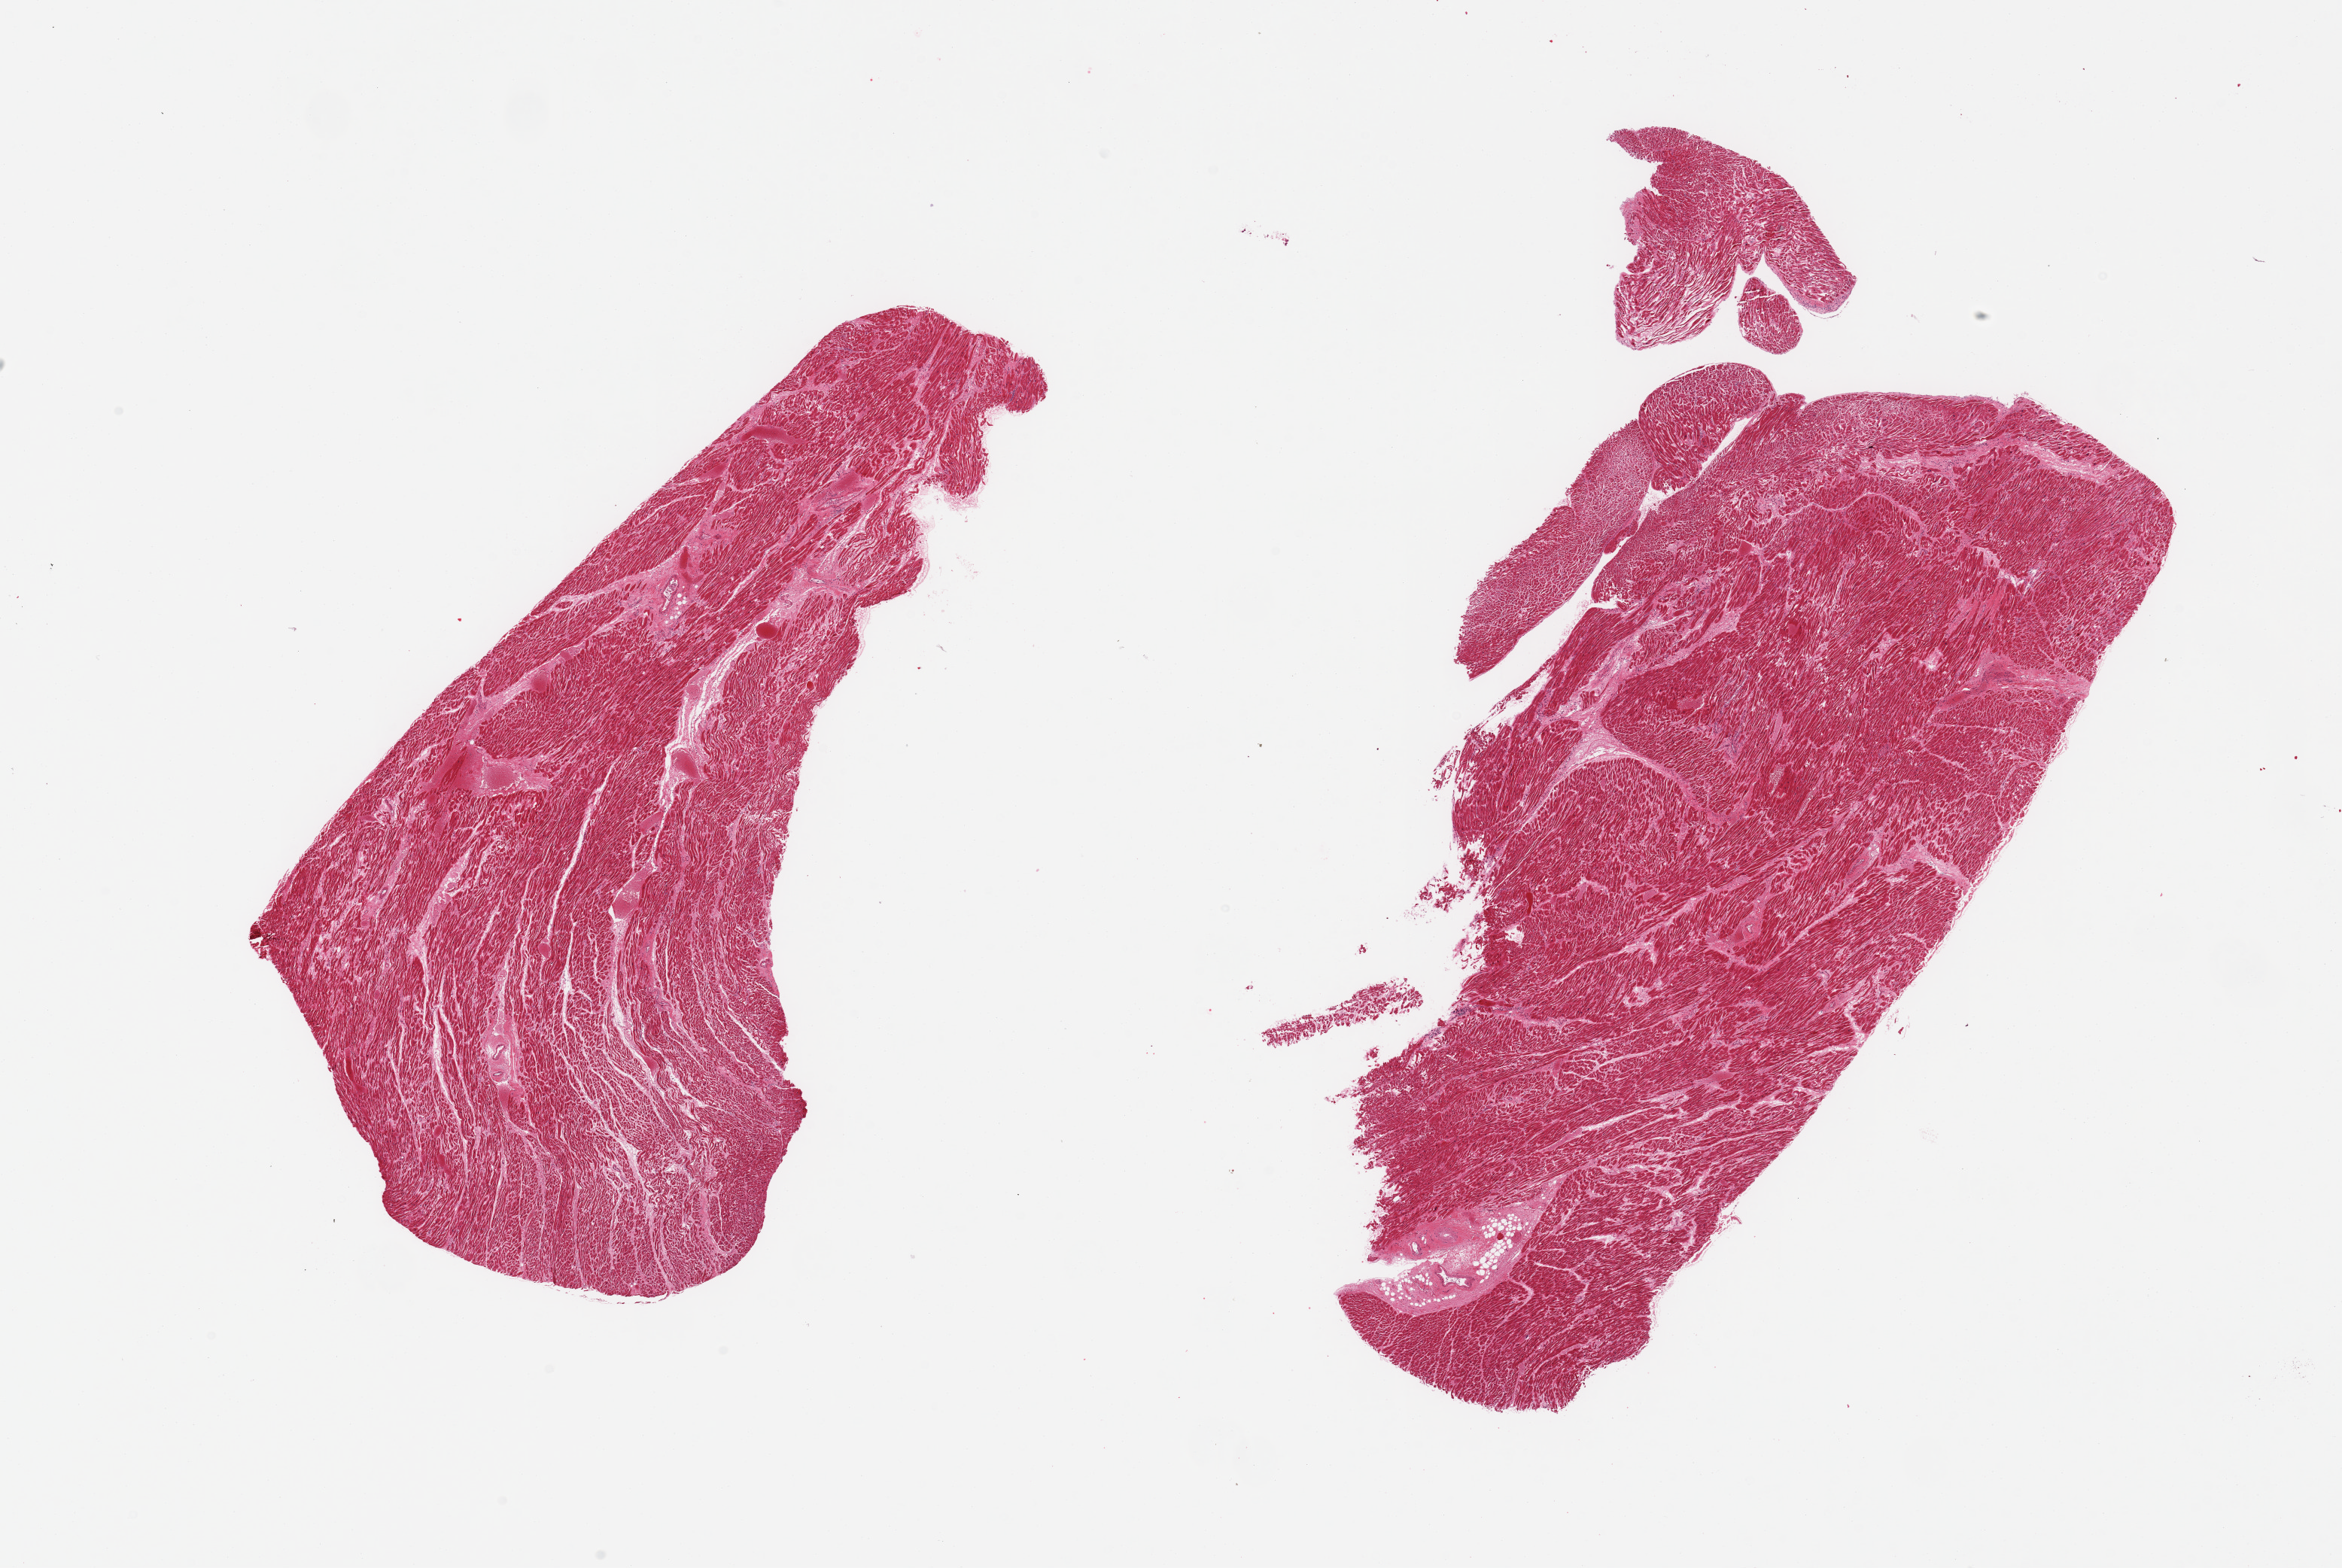
Haematoxylin and eosin whole-slide image, brightfield — shown as a low-resolution overview of the whole scanned area (about 24.6 x 16.5 mm, acquisition: 20x scan). PAXgene-fixed paraffin-embedded (PFPE) section. Target tissue: heart. Donor tissue sample. Male donor.
Review note (as recorded): 2 pieces; small foci of muscle drop-out & fibrosis consistent with past ischemia; patchy hypereosinophilia consistent with recent ischemia.